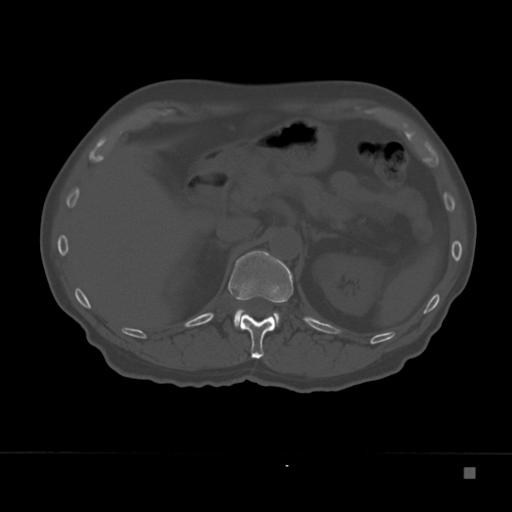
CT including the spine, one axial slice. Position 126 of 332 along the scan axis. Reconstruction kernel Br40s. 120 kVp. Bone window (W 1800 / L 400 HU). 1.5 mm slice thickness. 512 × 512 image matrix, field of view 389 × 389 mm. Patient: male, 72 years. From the clinical record (not read from this slice): primary cancer: skeletal.
Annotated regions visible in this slice (semi-automatically segmented with operator editing):
- L1 vertebra: box from (x=234, y=309) to (x=281, y=328) px
- T12 vertebra: (x=228, y=251)–(x=294, y=359)